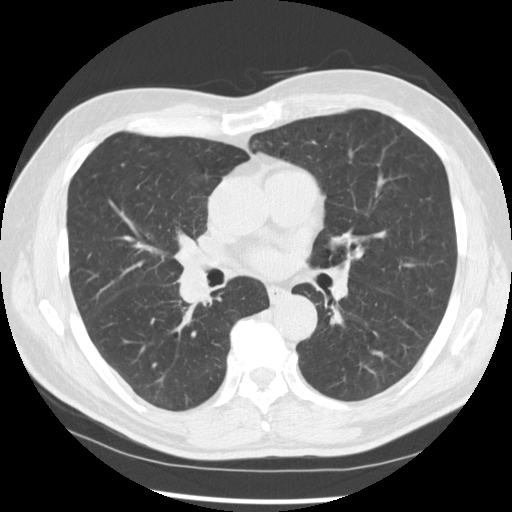
Low-dose screening chest CT, axial slice; baseline screening round; lung window (W 1500 / L -600 HU); 2.5 mm slice thickness; slice 152 of 277 in the series. Male, age 67 years at enrolment.
Expert reader's lesion annotation, box from (x=160, y=248) to (x=229, y=312) px. The exam's reader record, not a measurement of the box and not confirmed to be the same lesion: non-calcified nodule or mass ≥4 mm, left lower lobe, 15 × 15 mm, spiculated (stellate) margins, soft tissue attenuation. Note: the box lies in the patient's right hemithorax on this image, whereas the reader's record names the left lung; they may be different findings. Official screen result: positive, change unspecified: nodule(s) >= 4 mm or enlarging nodule(s), mass(es), or other non-specific abnormalities suspicious for lung cancer. Later outcome: lung cancer diagnosed 49 days after this screen — squamous cell carcinoma, NOS, right middle lobe, poorly differentiated (G3), stage IIB (AJCC 6th edition), 35 mm at pathology.